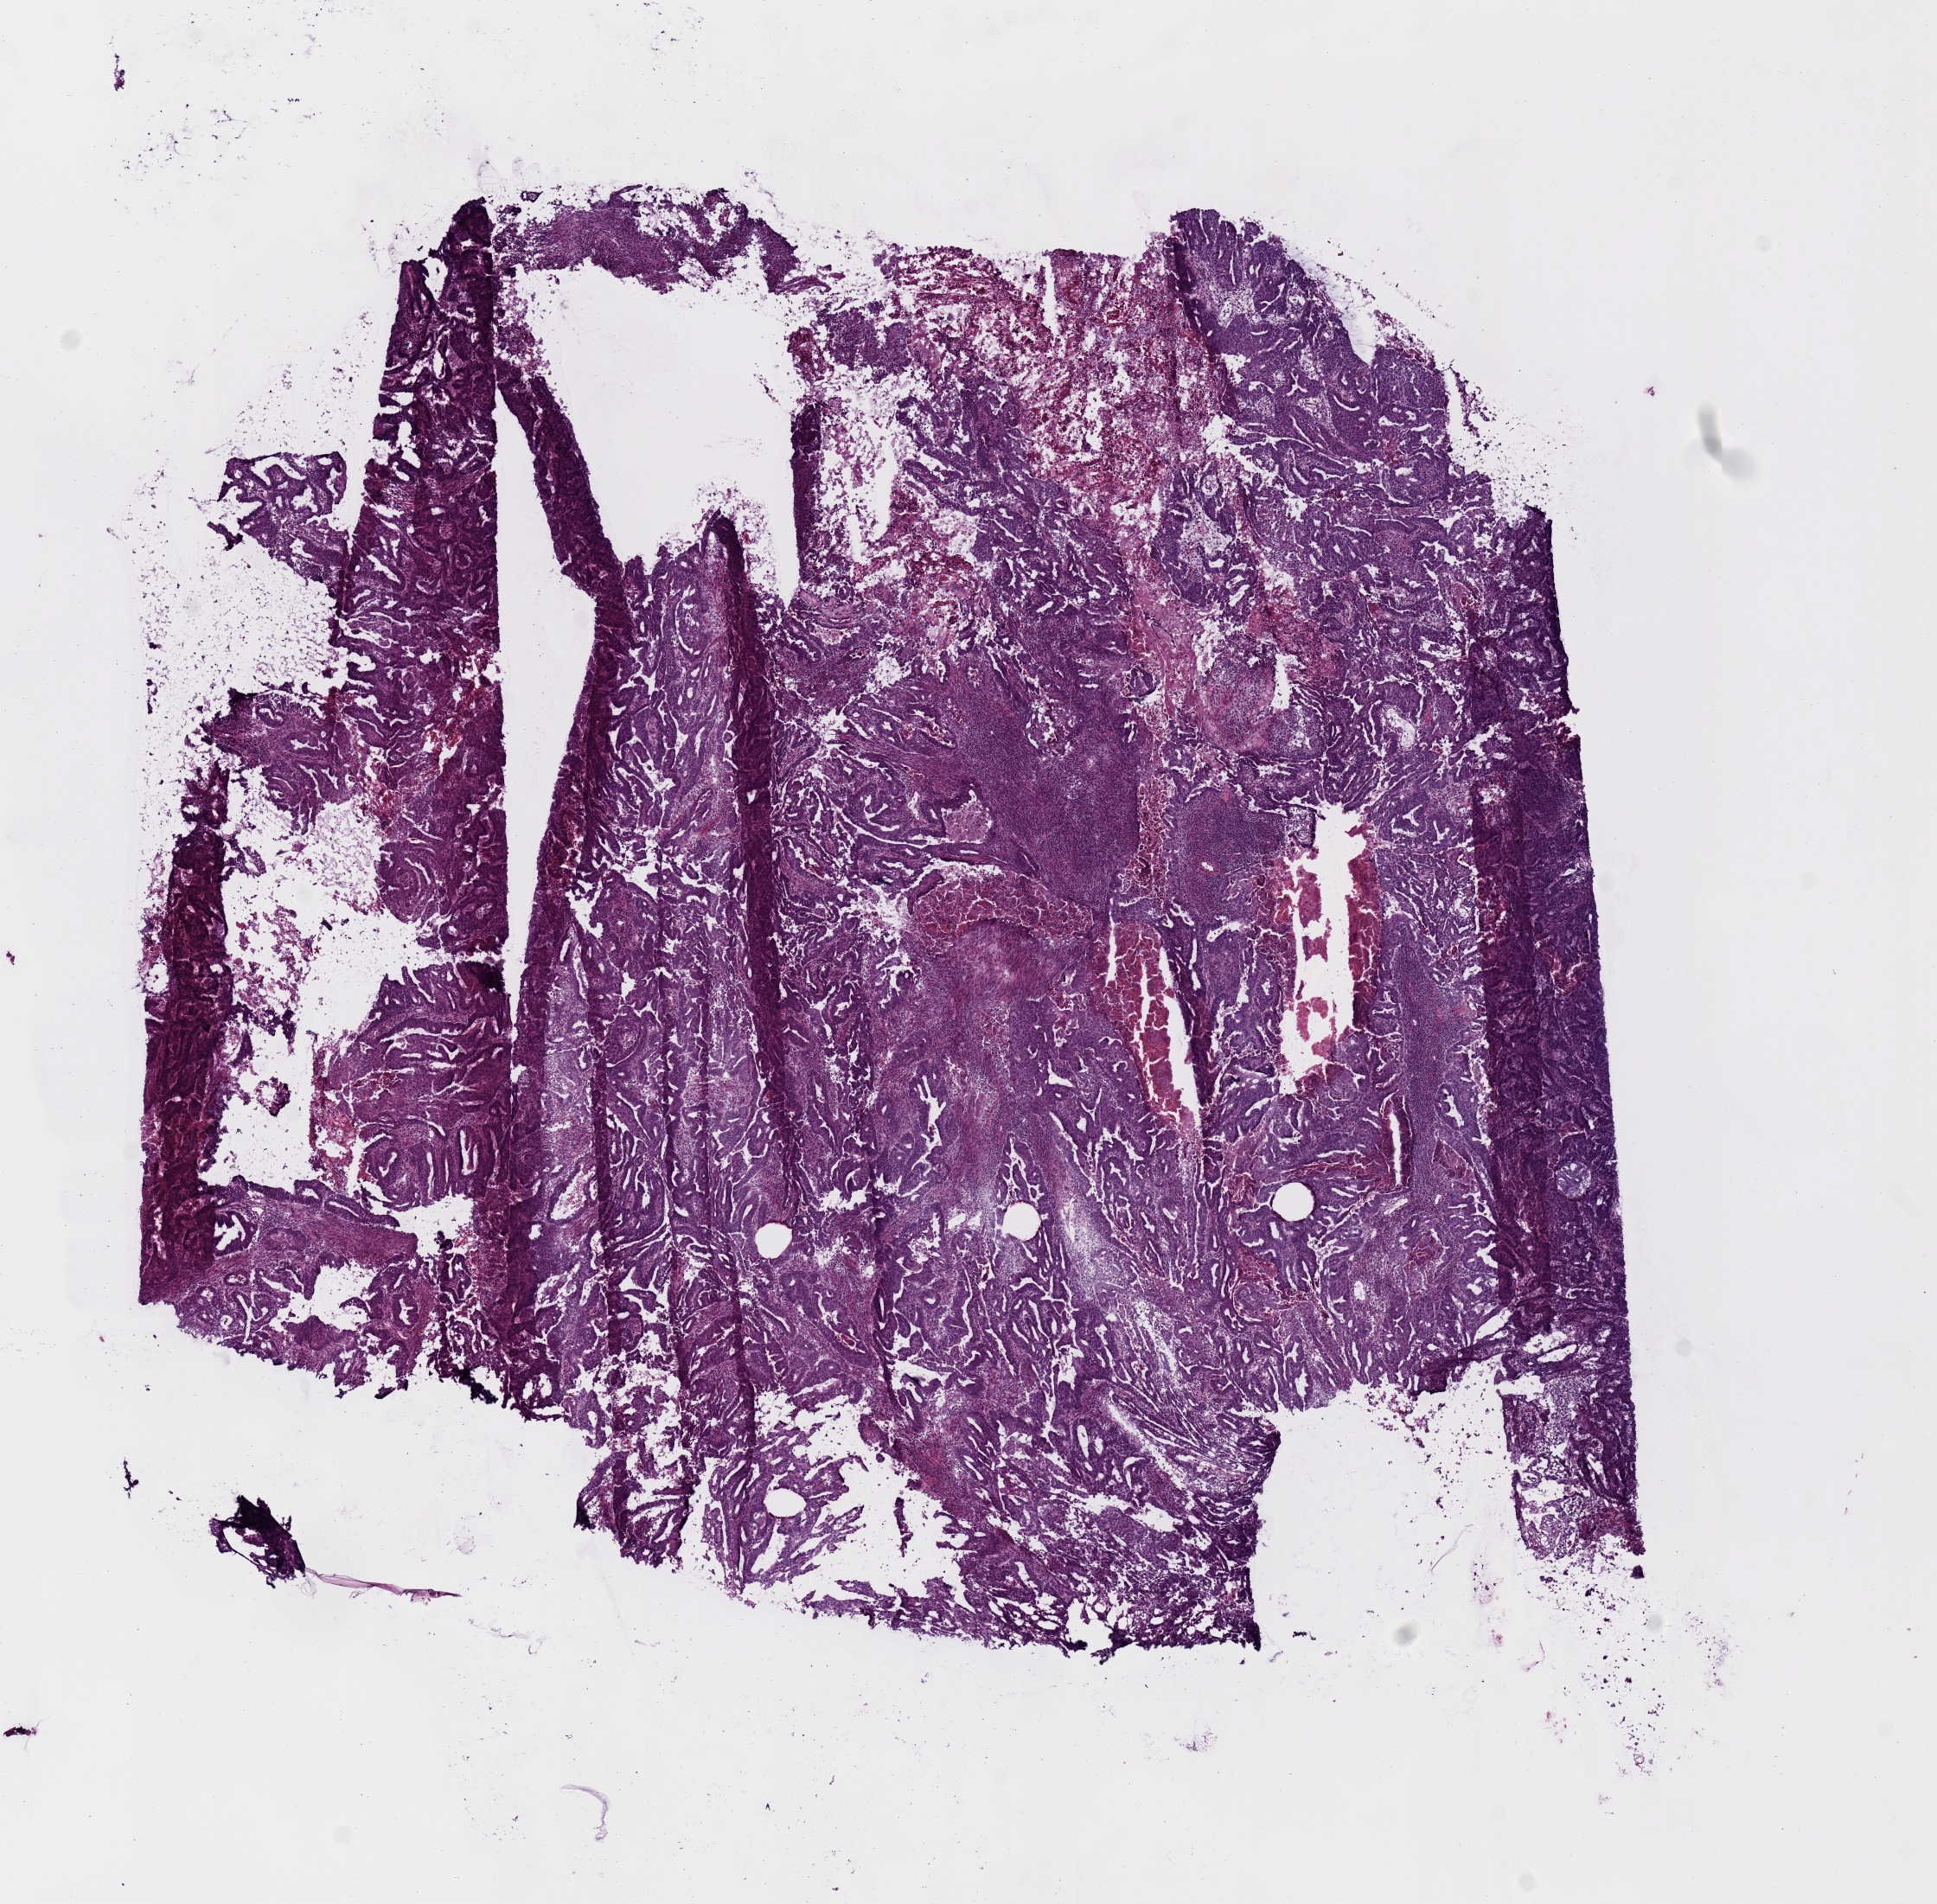
H&E whole-slide image — shown as a low-resolution overview of the whole scanned area (about 8.9 x 8.7 mm); frozen section from the top of the tissue portion; sample: primary tumour, uterus. Patient: female, age at initial diagnosis 46 years.
Histologic diagnosis: Endometrioid adenocarcinoma, NOS (endometrium).